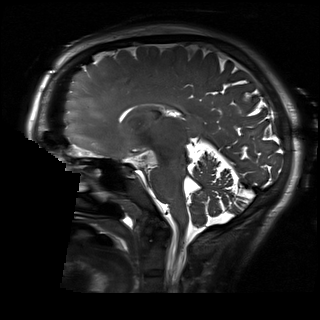
Brain MRI from a brain-tumour surgery series, one sagittal slice. 1 mm slice thickness. 320 × 320 image matrix, field of view 230 × 230 mm. Case-level facts recorded for this patient, not image findings: histopathology: Glioblastoma; WHO grade: 2; IDH mutation: no; tumour location: Right Skull Base Temporal.
Annotated regions visible in this slice (outlined manually by an expert reader):
- residual tumour: bounding box [x1, y1, x2, y2] px = [149, 156, 154, 161]